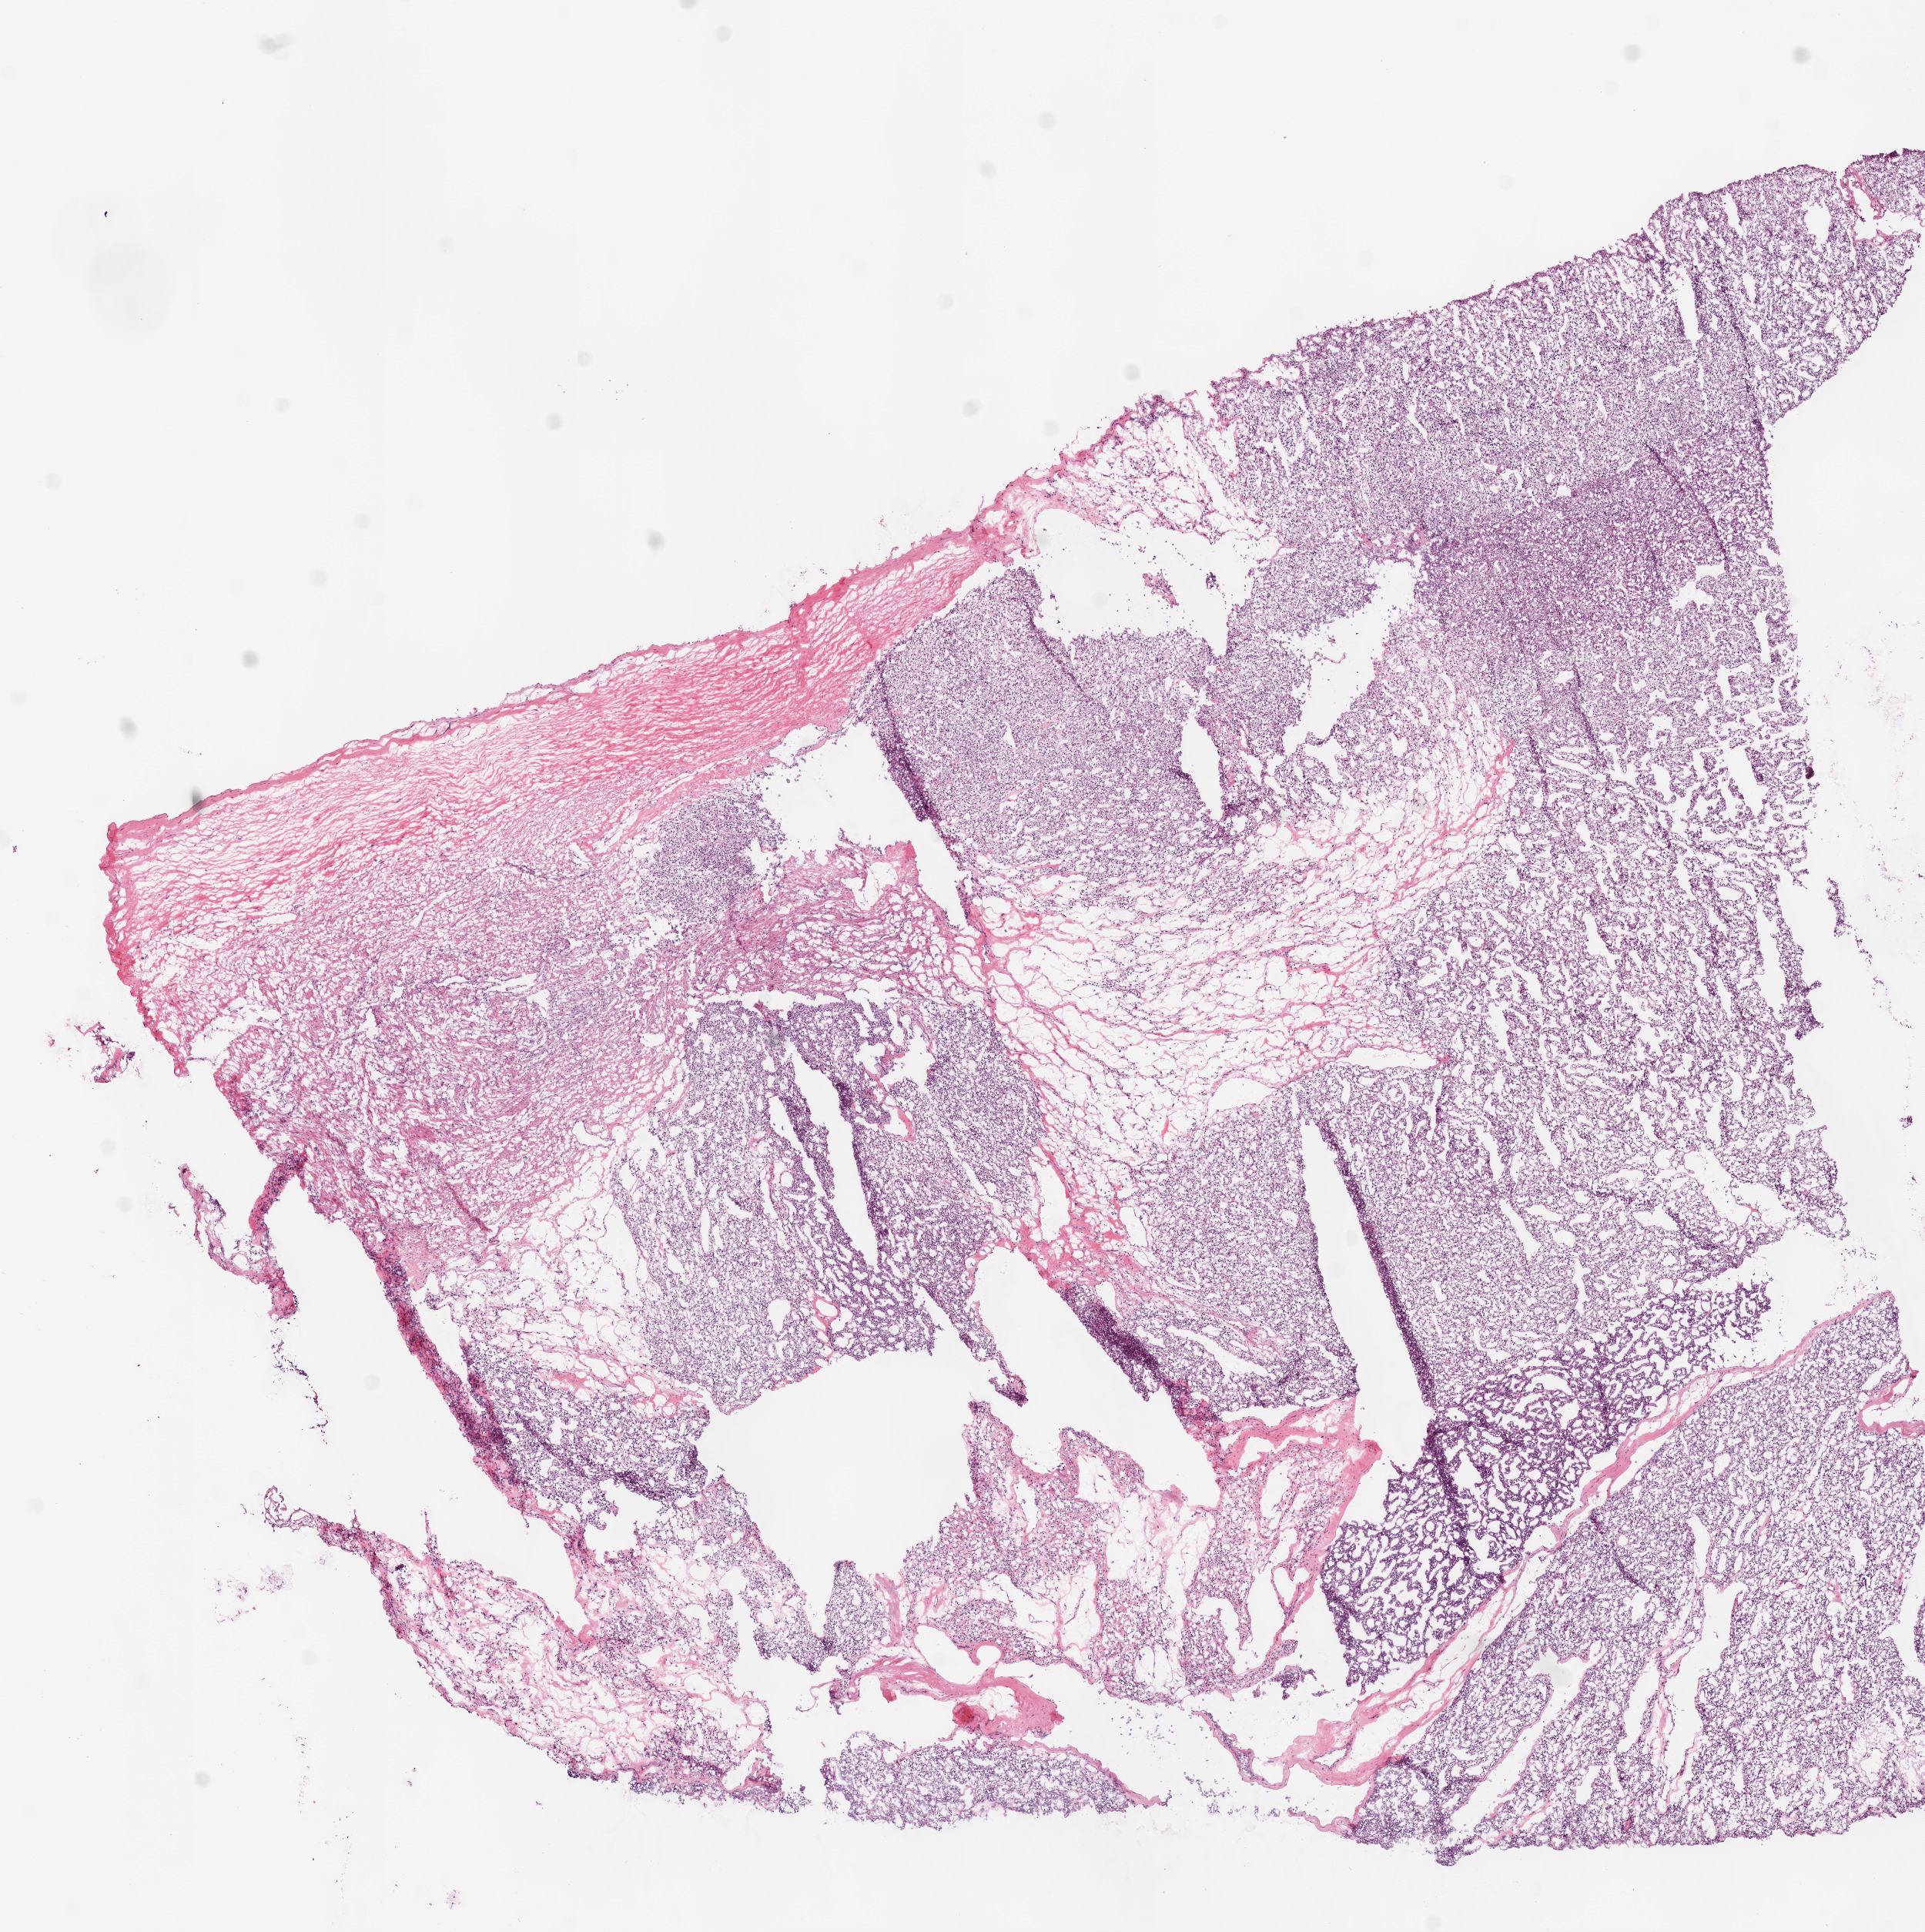
H&E-stained whole-slide image, a low-resolution overview of the entire scanned area, about 10.0 x 10.1 mm (from a 20x scan); frozen section; primary tumour sample from the kidney. Male patient; age at initial diagnosis 72 years. Histologic grade: G2 (moderately differentiated). Slide review estimates, as recorded: tumour cells 85%, tumour nuclei 80%, normal cells 0%, stromal cells 15%, necrosis 0%.
AJCC pathologic stage: I. TNM: T1b NX M0. Pathologic diagnosis: Clear cell adenocarcinoma, NOS.